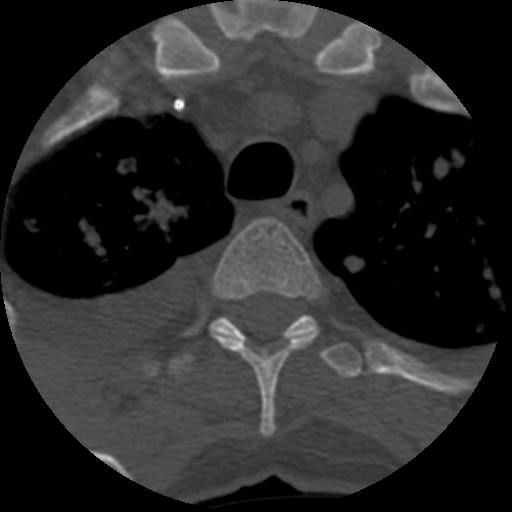
CT including the spine, one axial slice; slice 482 of 708 in the series (ordered by position); 120 kVp; one of 3 acquisitions stored at this slice position; bone window (W 1800 / L 400 HU); 512 × 512 image matrix. Patient age 55 years. Case-level facts recorded for this patient, not image findings: primary cancer: colon.
Annotated regions visible in this slice (semi-automatic segmentation, software-assisted and operator-edited):
- T3 vertebra: box from (x=210, y=218) to (x=320, y=437) px
- T4 vertebra: (x=168, y=314)–(x=363, y=380)